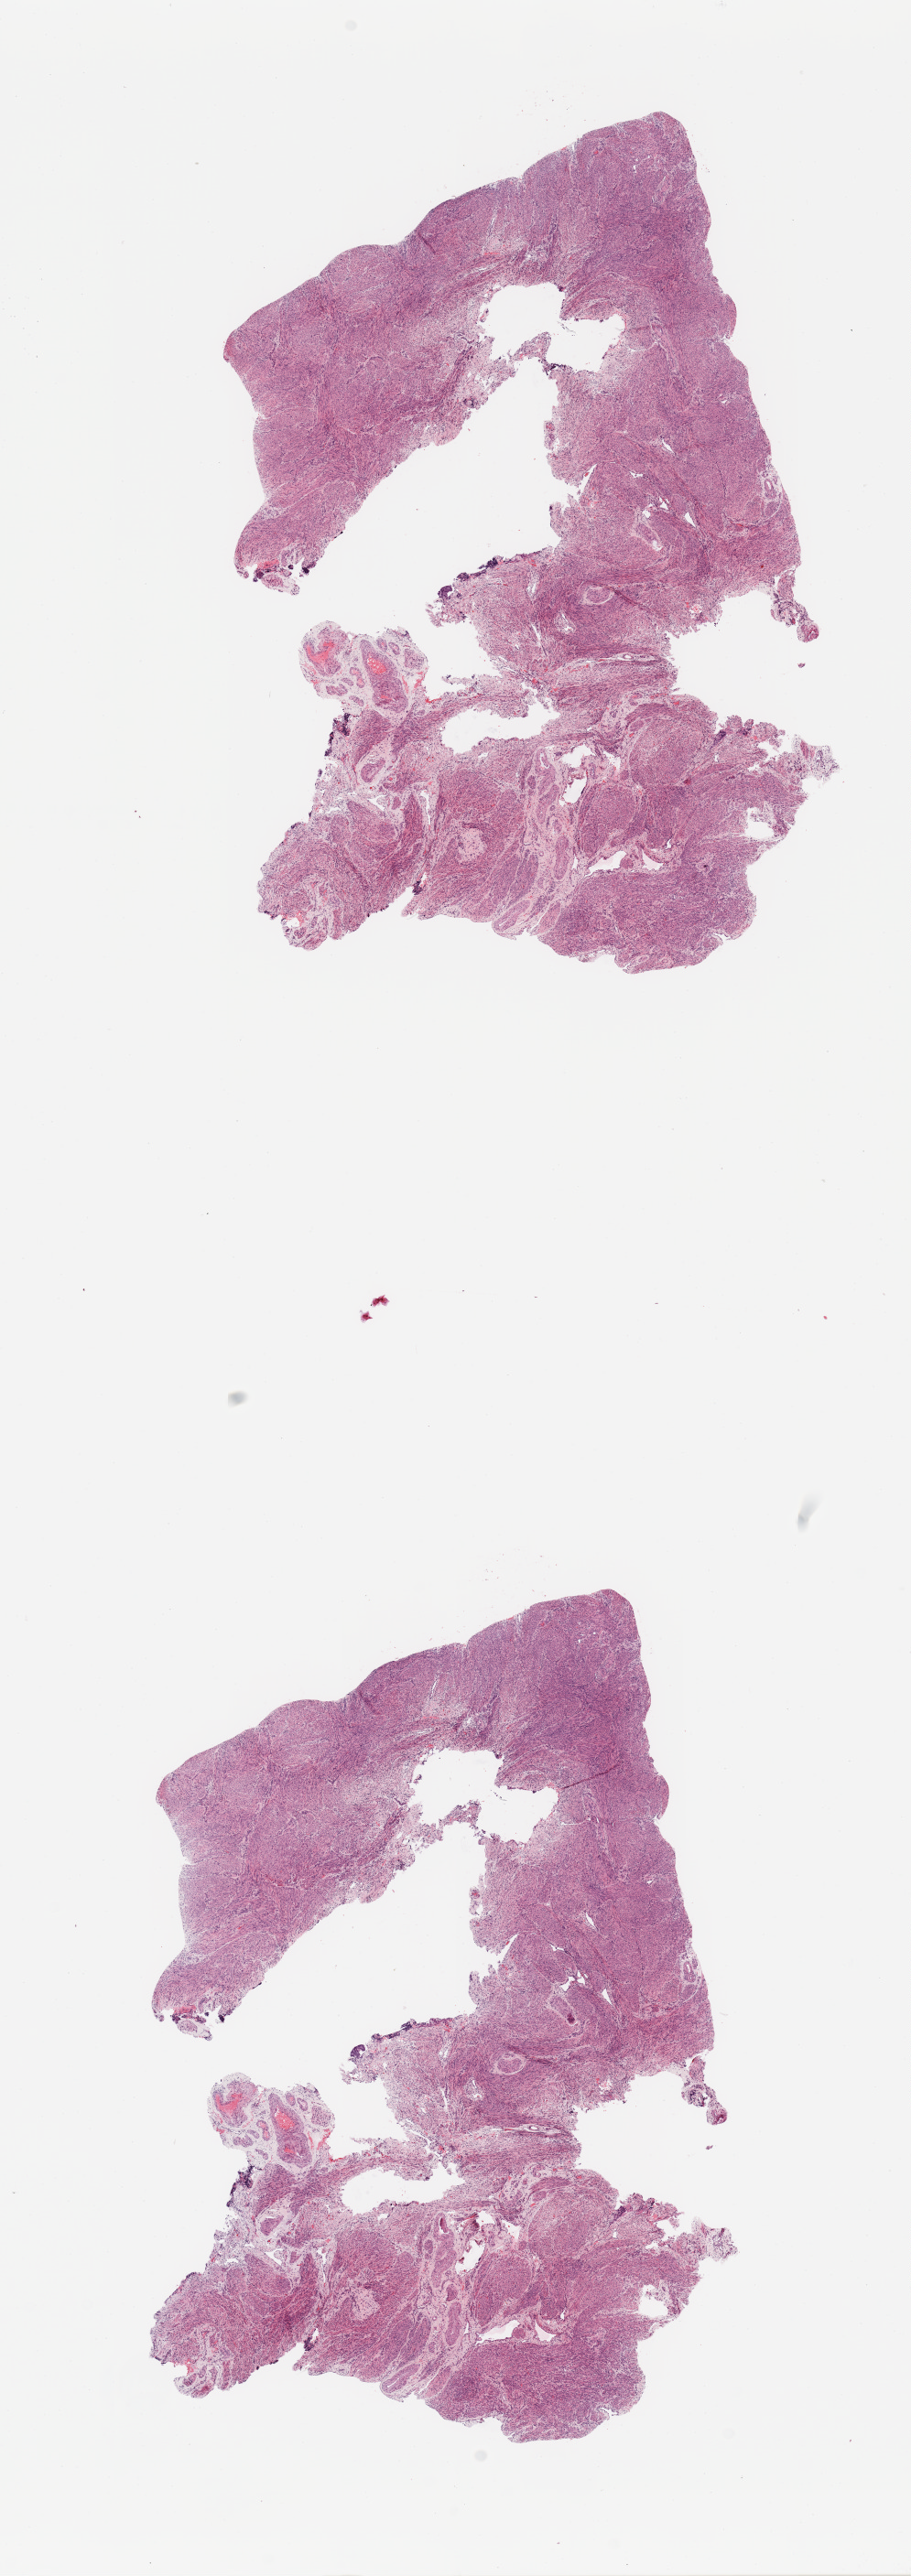
Digitized H&E-stained tissue section (whole slide) — shown as a low-resolution overview of the whole scanned area (about 7.9 x 22.3 mm, slide scanned at 20x), uterus, normal (non-tumour) tissue. Female, 60 y/o.
This section: normal (non-tumour) tissue from the same patient. Patient diagnosis: Endometrioid adenocarcinoma, NOS.